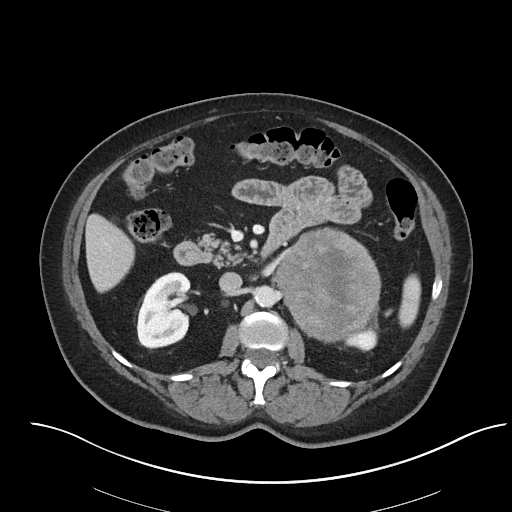
Contrast-enhanced abdominal CT, one axial slice. Slice 36 of 92 in the series (ordered by position). 120 kVp. Intravenous contrast given. Soft-tissue window (W 400 / L 40 HU). 3 mm slice thickness. 512 × 512 image matrix, field of view 440 × 440 mm. Female patient, age 53 years. Case-level facts recorded for this patient, not image findings: diagnosis: adrenocortical carcinoma; tumour side: left adrenal; tumour size at pathology: 9 cm; Ki-67 index: 28 %; stage (as recorded): 2.
Outlined on this slice (semi-automatic segmentation, software-assisted and operator-edited):
- mass: bounding box [x1, y1, x2, y2] px = [273, 229, 381, 339]